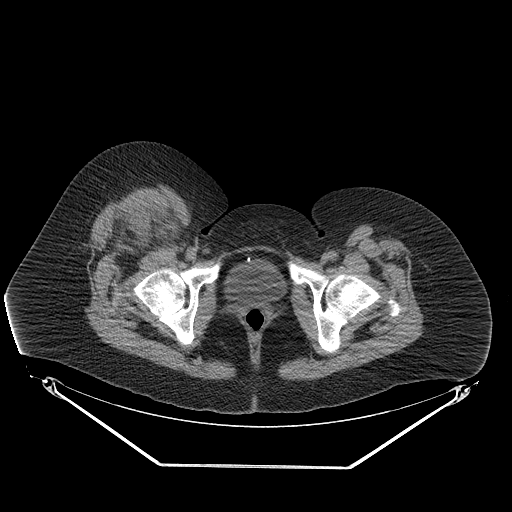
CT of an extremity soft-tissue mass (from a PET/CT study), one axial slice. Slice 65 of 267 in the series (ordered by position). Reconstruction kernel STANDARD. Soft-tissue window (W 400 / L 40 HU). 512 × 512 image matrix. Female patient. From the clinical record (not read from this slice): histological type: malignant solitary fibrous tumor; grade: intermediate; site of the primary tumour: right thigh.
Outlined on this slice (expert contour drawn on MRI and transferred to this co-registered scan by the dataset authors):
- gross tumour volume including surrounding oedema: bounding box (x1, y1, x2, y2) in pixels: (105, 201, 170, 243)